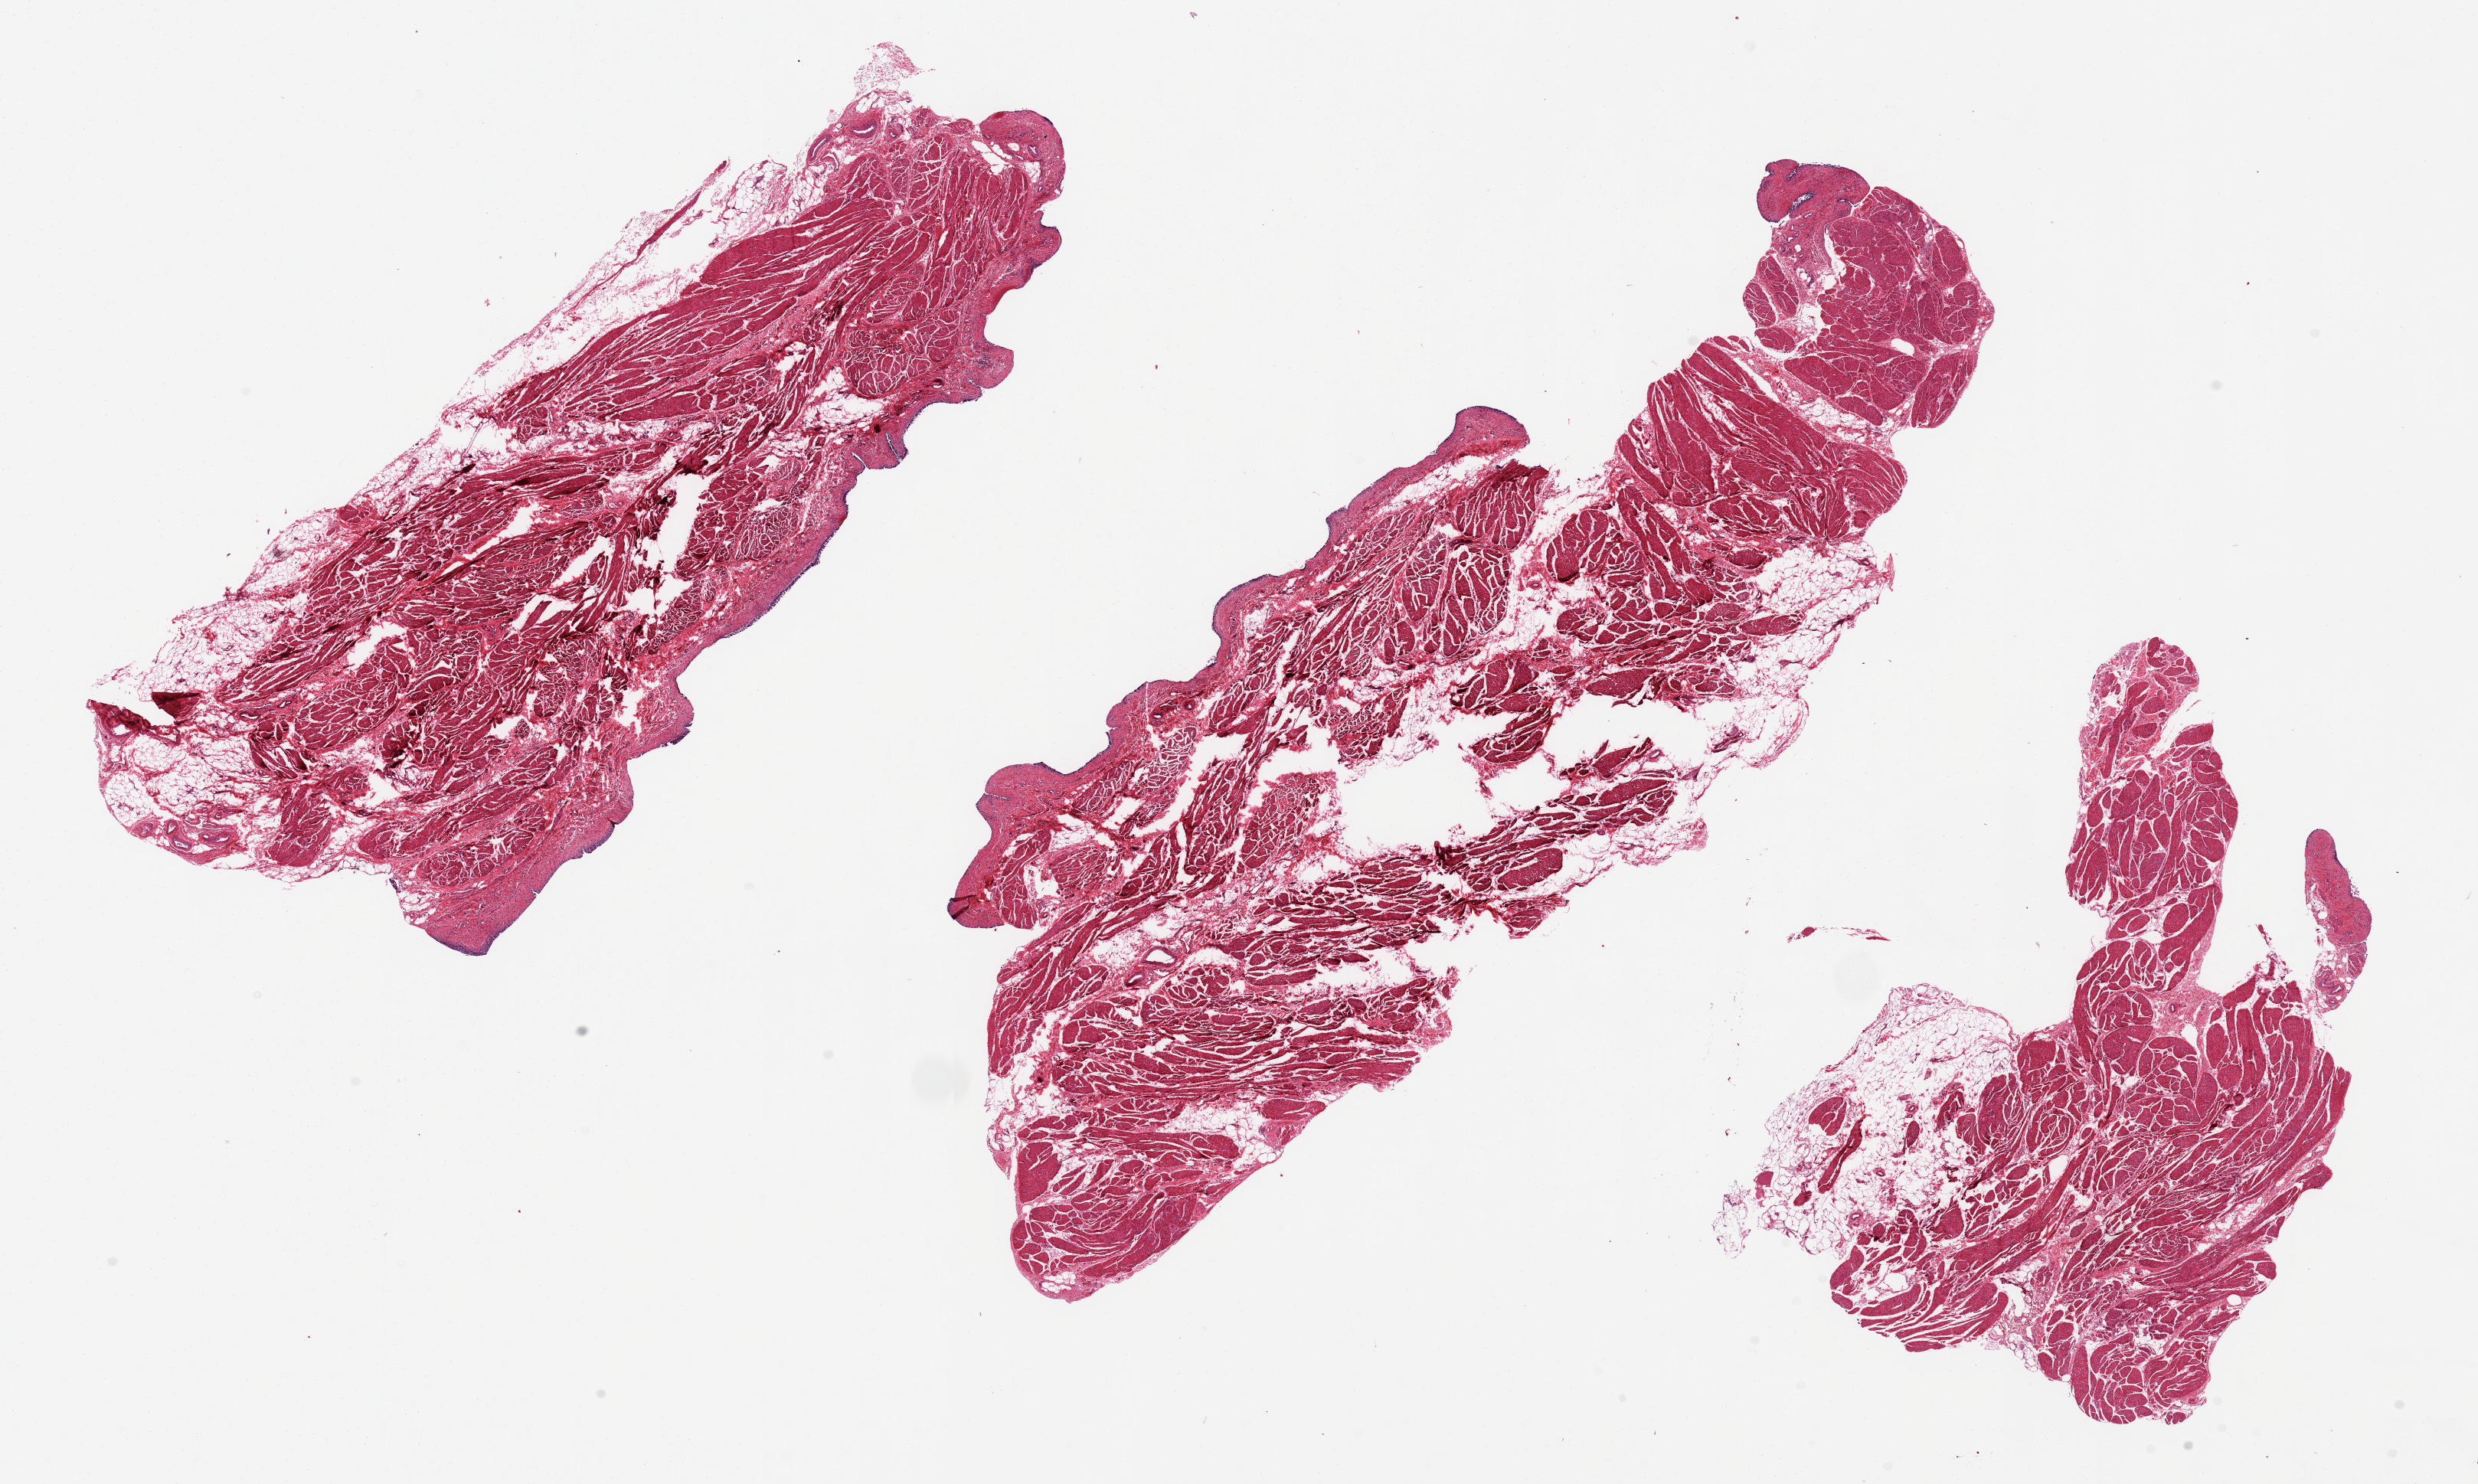
H&E whole-slide image, a low-resolution overview of the entire scanned area, about 25.6 x 15.3 mm (slide scanned at 20x); PAXgene-fixed, paraffin-embedded tissue; target tissue: urinary bladder; donor tissue sample. Donor: male.
Review note (as recorded): Mucosa largely sloughed. Muscle has mild autolysis.